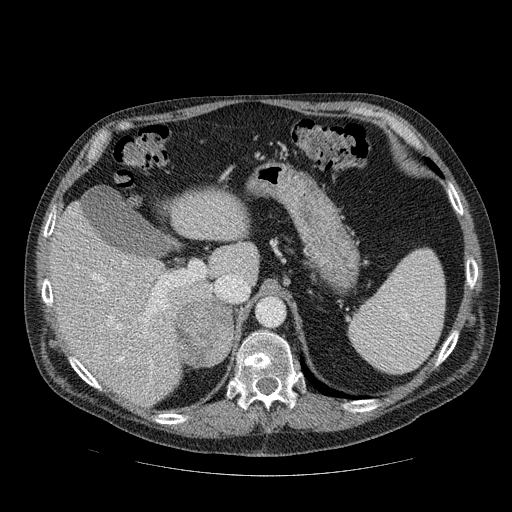
Contrast-enhanced abdominal CT, one axial slice; slice 66 of 111 in the series (ordered by position); 120 kVp; soft-tissue window (W 400 / L 40 HU); 512 × 512 image matrix, field of view 420 × 420 mm. Patient: male, 56 years. Case-level facts recorded for this patient, not image findings: diagnosis: adrenocortical carcinoma; tumour side: right adrenal; tumour size at pathology: 9 cm; Ki-67 index: 48 %; stage (as recorded): 4.
Outlined on this slice (semi-automatic segmentation, software-assisted and operator-edited):
- mass: bounding box [x1, y1, x2, y2] px = [175, 300, 233, 365]